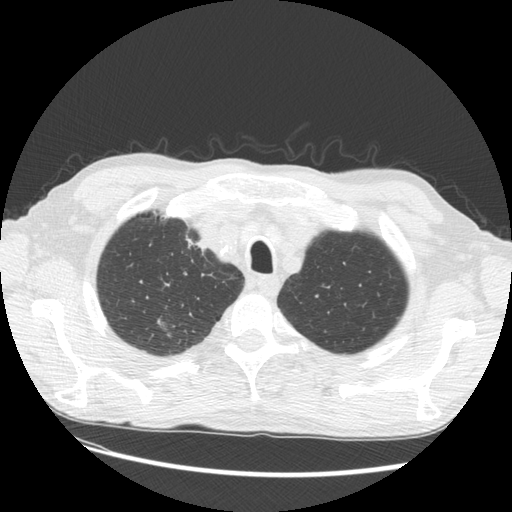
Low-dose screening chest CT, one axial slice; position 117 of 133 along the scan axis; reconstruction kernel STANDARD; lung window (W 1500 / L -600 HU); 2.5 mm slice thickness; 512 × 512 image matrix, field of view 360 × 360 mm.
Annotated regions visible in this slice (expert manual segmentation):
- lesion 2 (tumor, upper lobe of right lung): bounding box (x1, y1, x2, y2) in pixels: (156, 319, 173, 339)